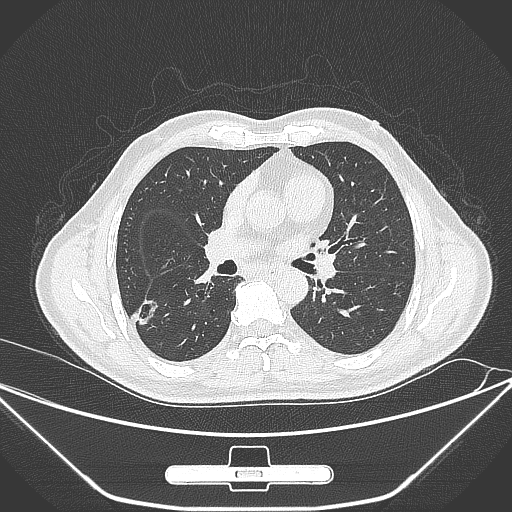
Chest CT, one axial slice. Position 155 of 310 along the scan axis. 120 kVp. Lung window (W 1500 / L -600 HU). 1 mm slice thickness. 512 × 512 image matrix. Male patient, age 71 years. Case-level facts recorded for this patient, not image findings: clinical TNM (as recorded): T1c N0 M0; histopathological grade: G2.
Annotated regions visible in this slice (rectangle marked by the reading radiologist):
- lung tumour (recorded histology: adenocarcinoma): bounding box <133,292,160,328> (left, top, right, bottom; pixels)